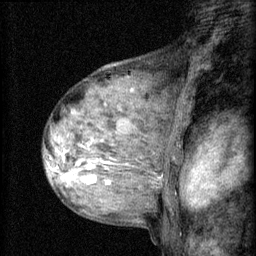
Breast MRI (dynamic contrast-enhanced), one sagittal slice. Slice 41 of 60 in the series (ordered by position). 3 images stored at this slice position (order not interpretable as contrast timing). 1.5 T. TE 4.2 ms, TR 8.2 ms. 2 mm slice thickness. 256 × 256 image matrix. Female patient, age 48 years.
Annotated regions visible in this slice (semi-automatic segmentation, software-assisted and operator-edited):
- analysis volume of interest (the breast-tissue region the enhancement analysis was run in; not a lesion): bounding box (x1, y1, x2, y2) in pixels: (54, 138, 133, 191)
- tumour enhancement mask (voxels above the 70 % enhancement threshold inside the analysis volume of interest): (56, 154, 111, 185)